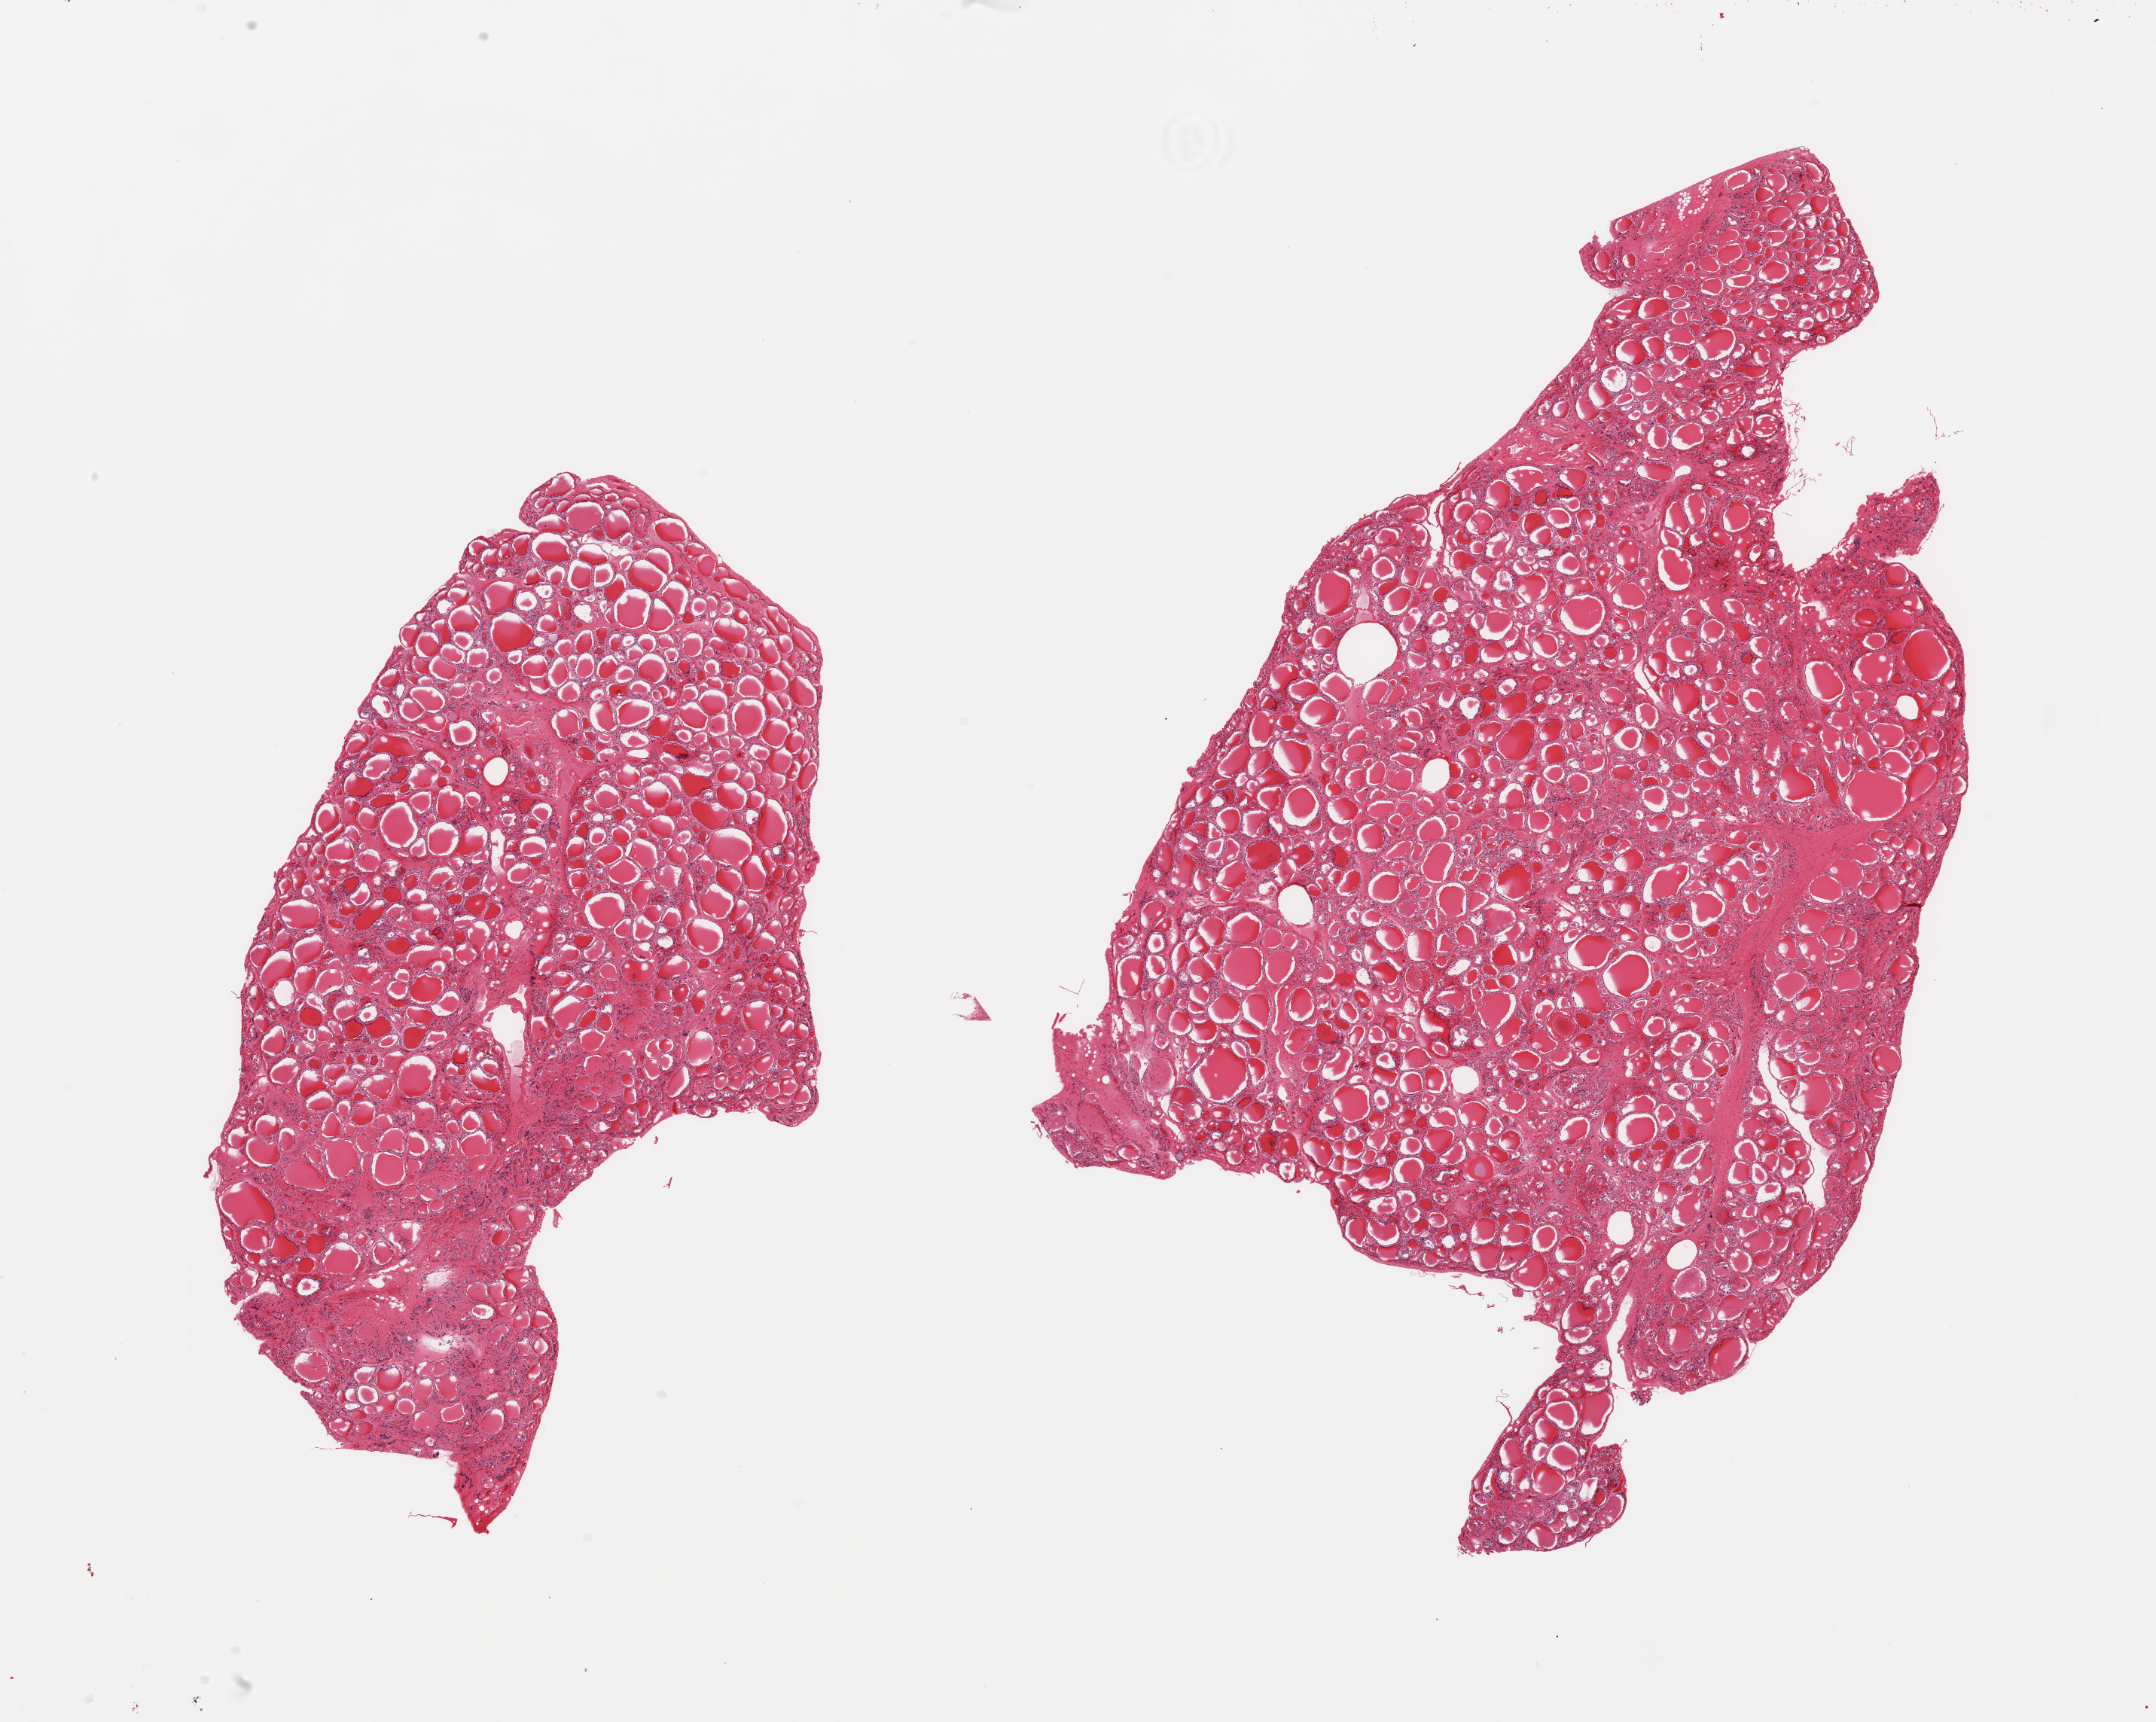
Digitized haematoxylin and eosin-stained section, brightfield — low-resolution overview of the scanned area, about 22.6 x 18.1 mm; PAXgene-fixed paraffin-embedded (PFPE) section; sampled site (target tissue): thyroid; donor tissue sample. Donor: male.
Review note (as recorded): 2 pieces.